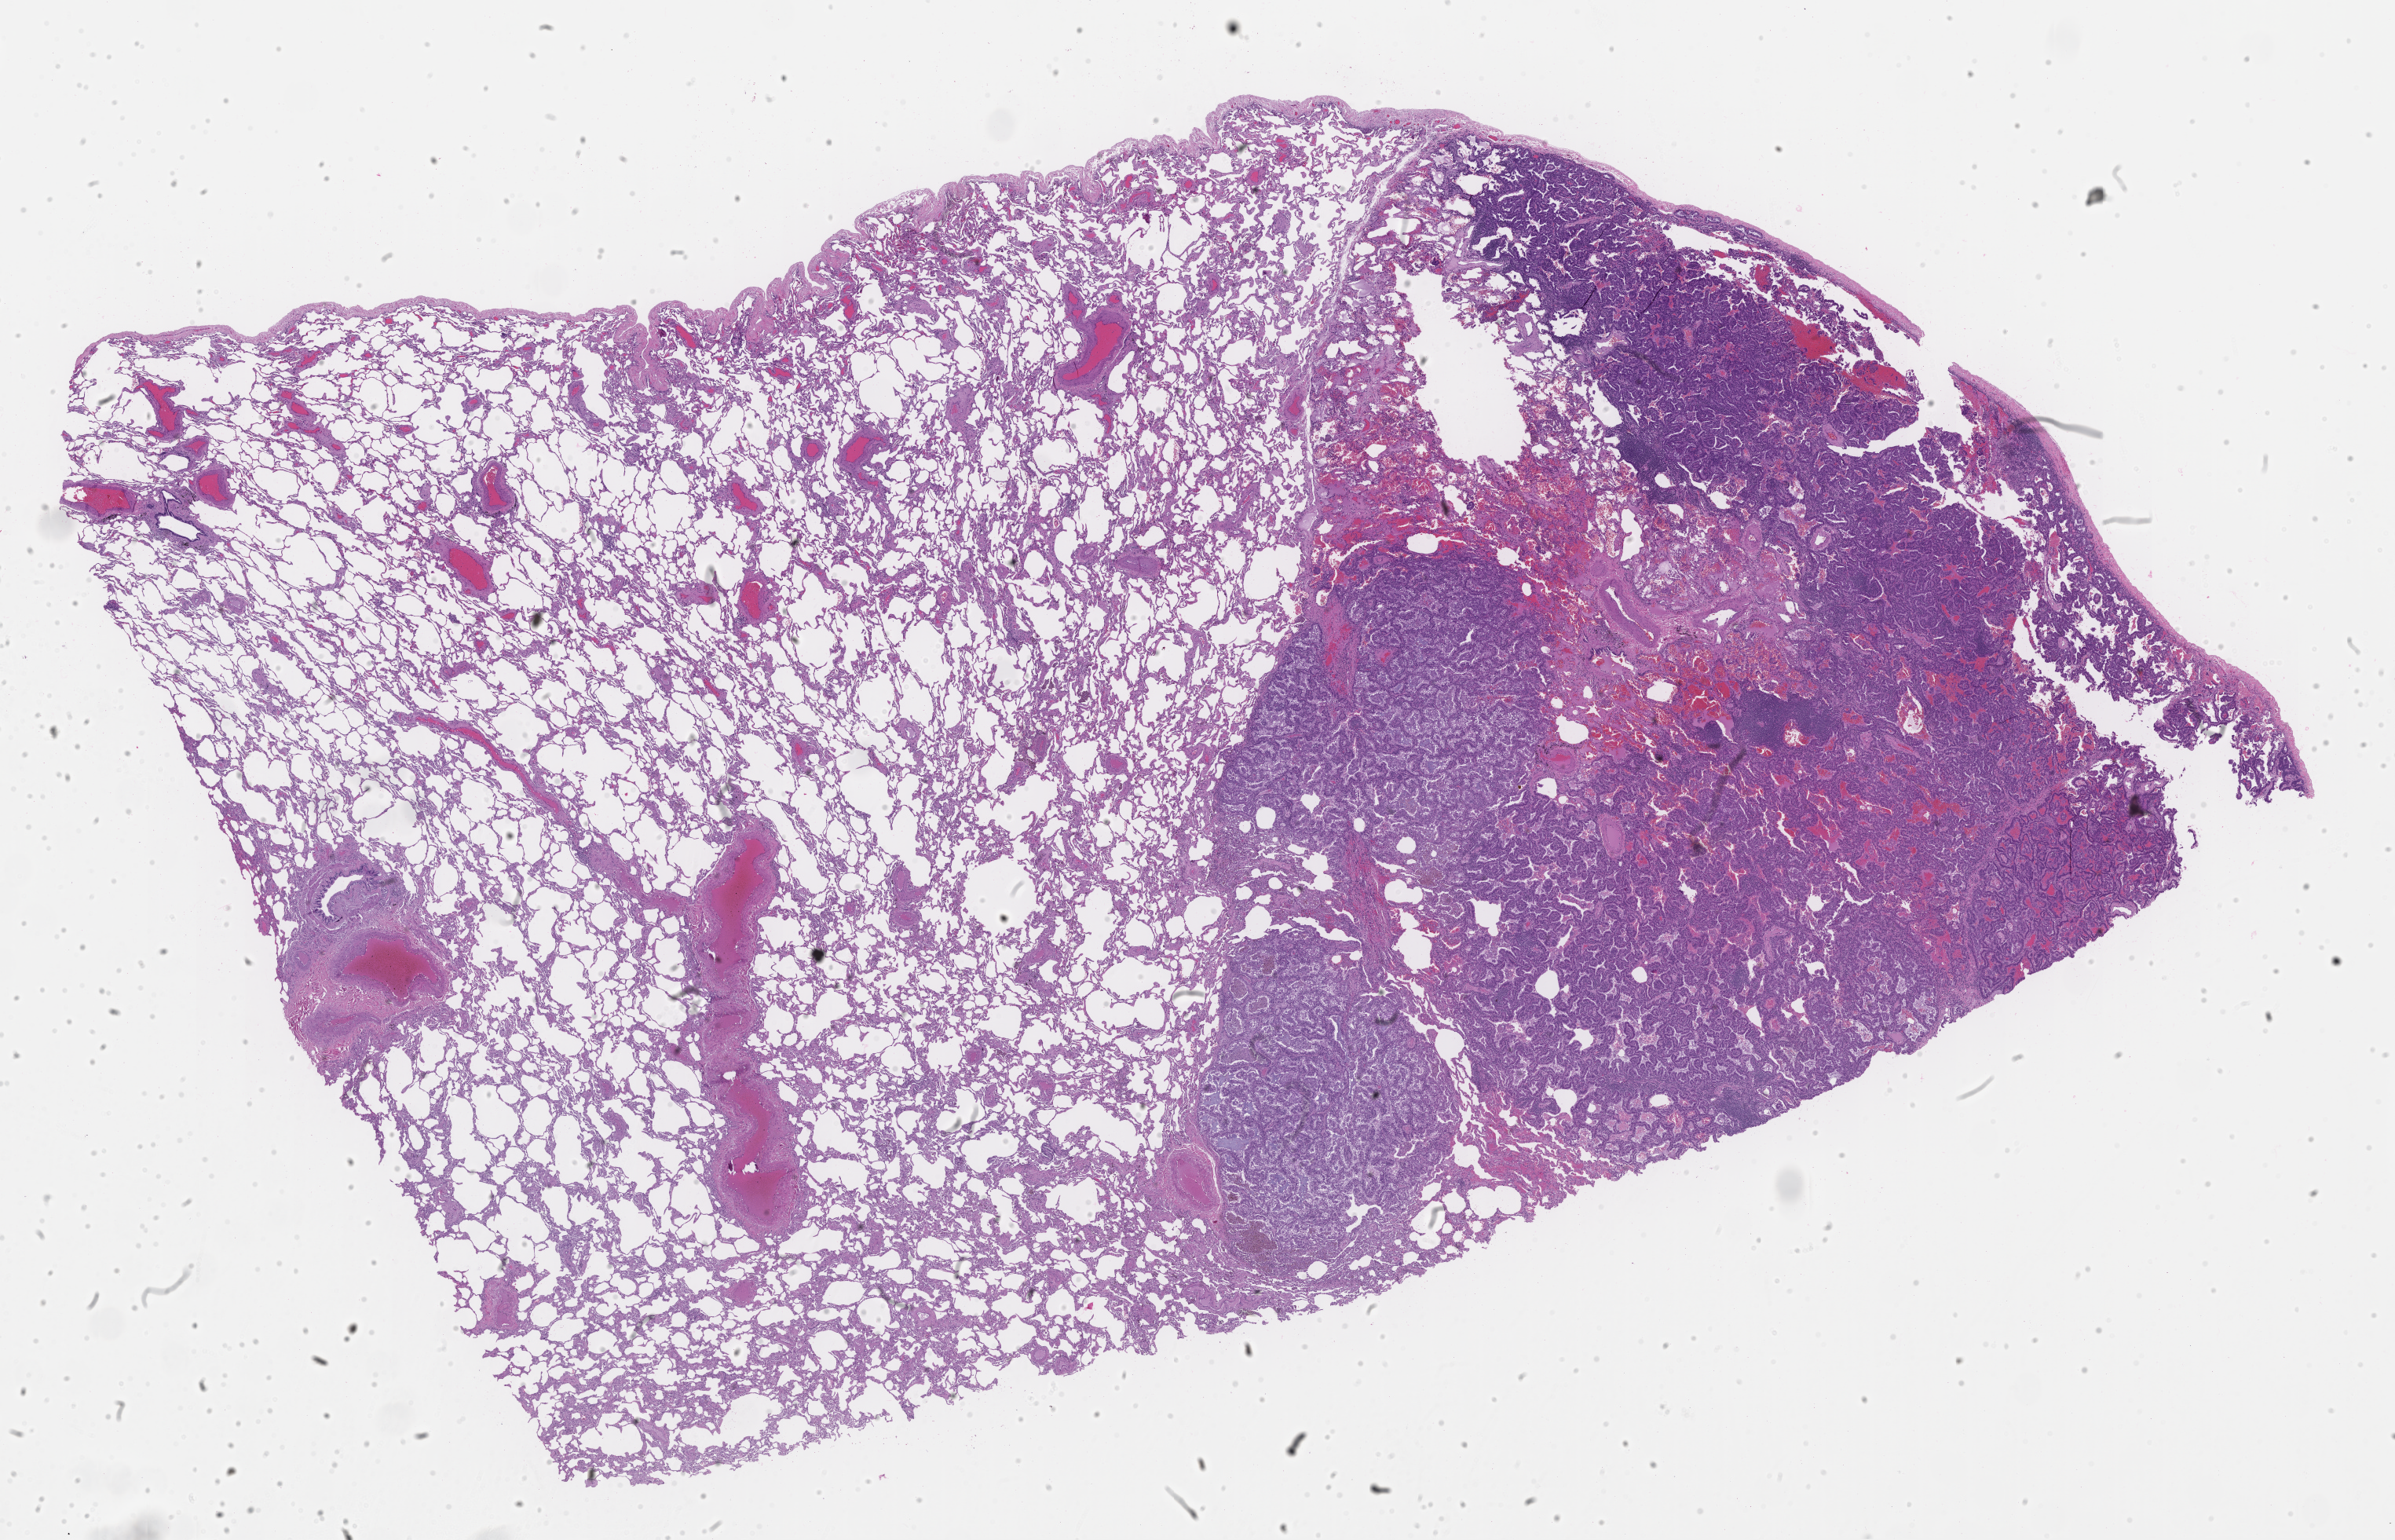
Digitized Hematoxylin and eosin (H&E) stained tissue section (whole slide) — a low-resolution overview of the entire scanned area, about 24.6 x 15.8 mm, tumour tissue sample, sampled site: lung. Male, 57 y/o. Histologic grade: G2 (moderately differentiated). Slide review estimates, as recorded: tumour nuclei 55%, necrosis 0%.
• histologic diagnosis: Adenocarcinoma, NOS
• AJCC pathologic stage: IA